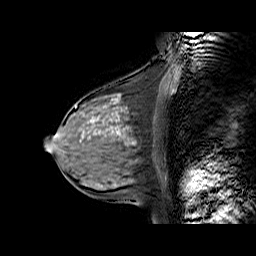
Breast MRI (dynamic contrast-enhanced), one sagittal slice; slice 28 of 60 in the series (ordered by position); dynamic contrast-enhanced series, time point 2 of 6 at this slice position (early post-contrast); 1.5 T; TE 6.3 ms, TR 32.9 ms; 256 × 256 image matrix, field of view 200 × 200 mm. Female patient. From the clinical record (not read from this slice): setting: breast cancer imaged before/during neoadjuvant chemotherapy; receptor status: HR-positive, HER2-negative.
Outlined on this slice (semi-automatic segmentation, software-assisted and operator-edited):
- analysis volume of interest (the breast-tissue region the enhancement analysis was run in; not a lesion): bounding box [x1, y1, x2, y2] px = [57, 86, 168, 170]
- tumour enhancement mask (voxels above the 100 % enhancement threshold inside the analysis volume of interest): [83, 98, 135, 144]